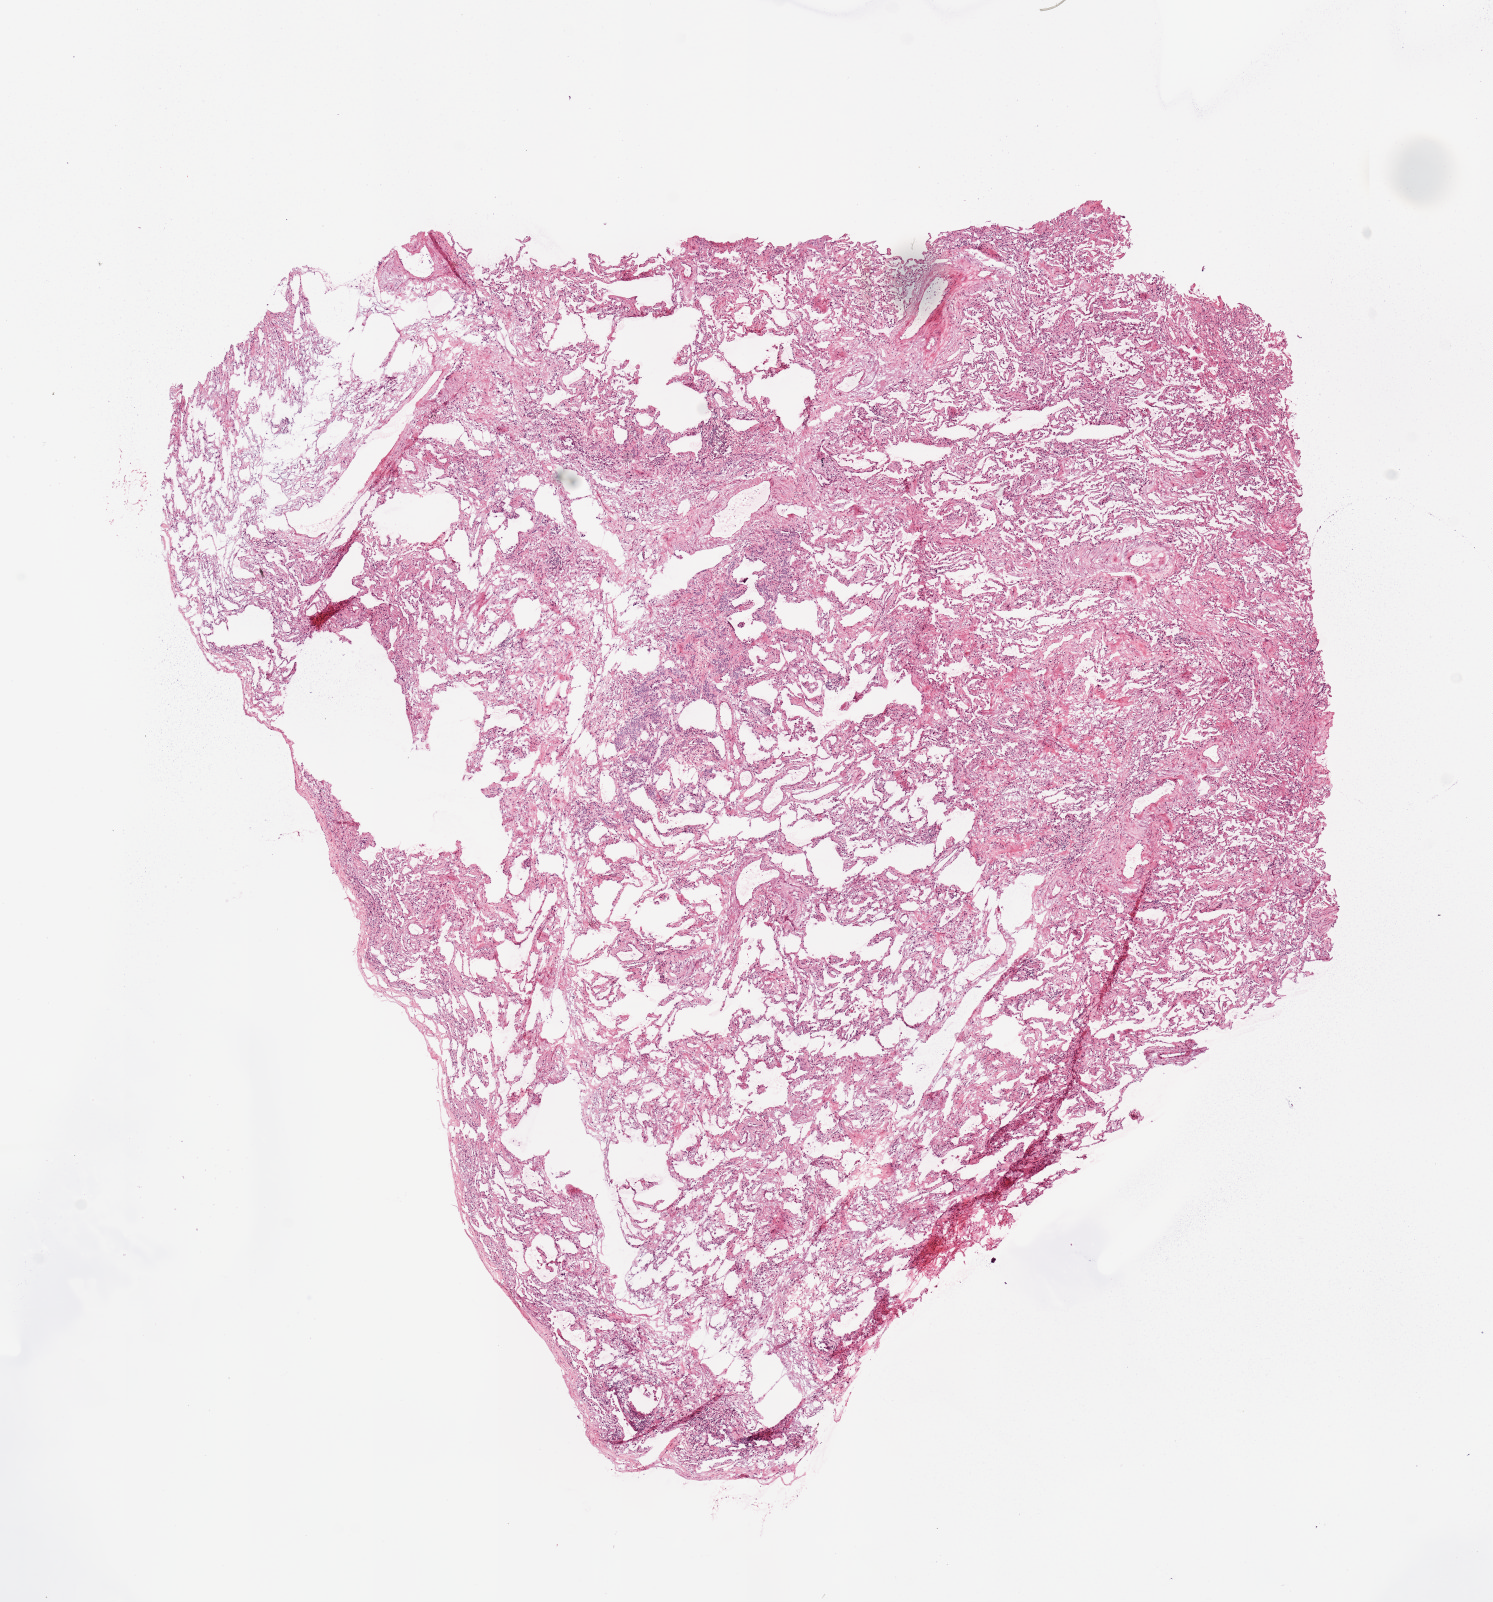
H&E whole-slide image — whole scanned area (about 11.8 x 12.7 mm, slide scanned at 20x) shown as a low-resolution overview; normal (non-tumour) tissue sample, sampled site: lung. Female, 80 y/o.
* this section: normal (non-tumour) tissue from the same patient
* patient diagnosis: Adenocarcinoma, NOS